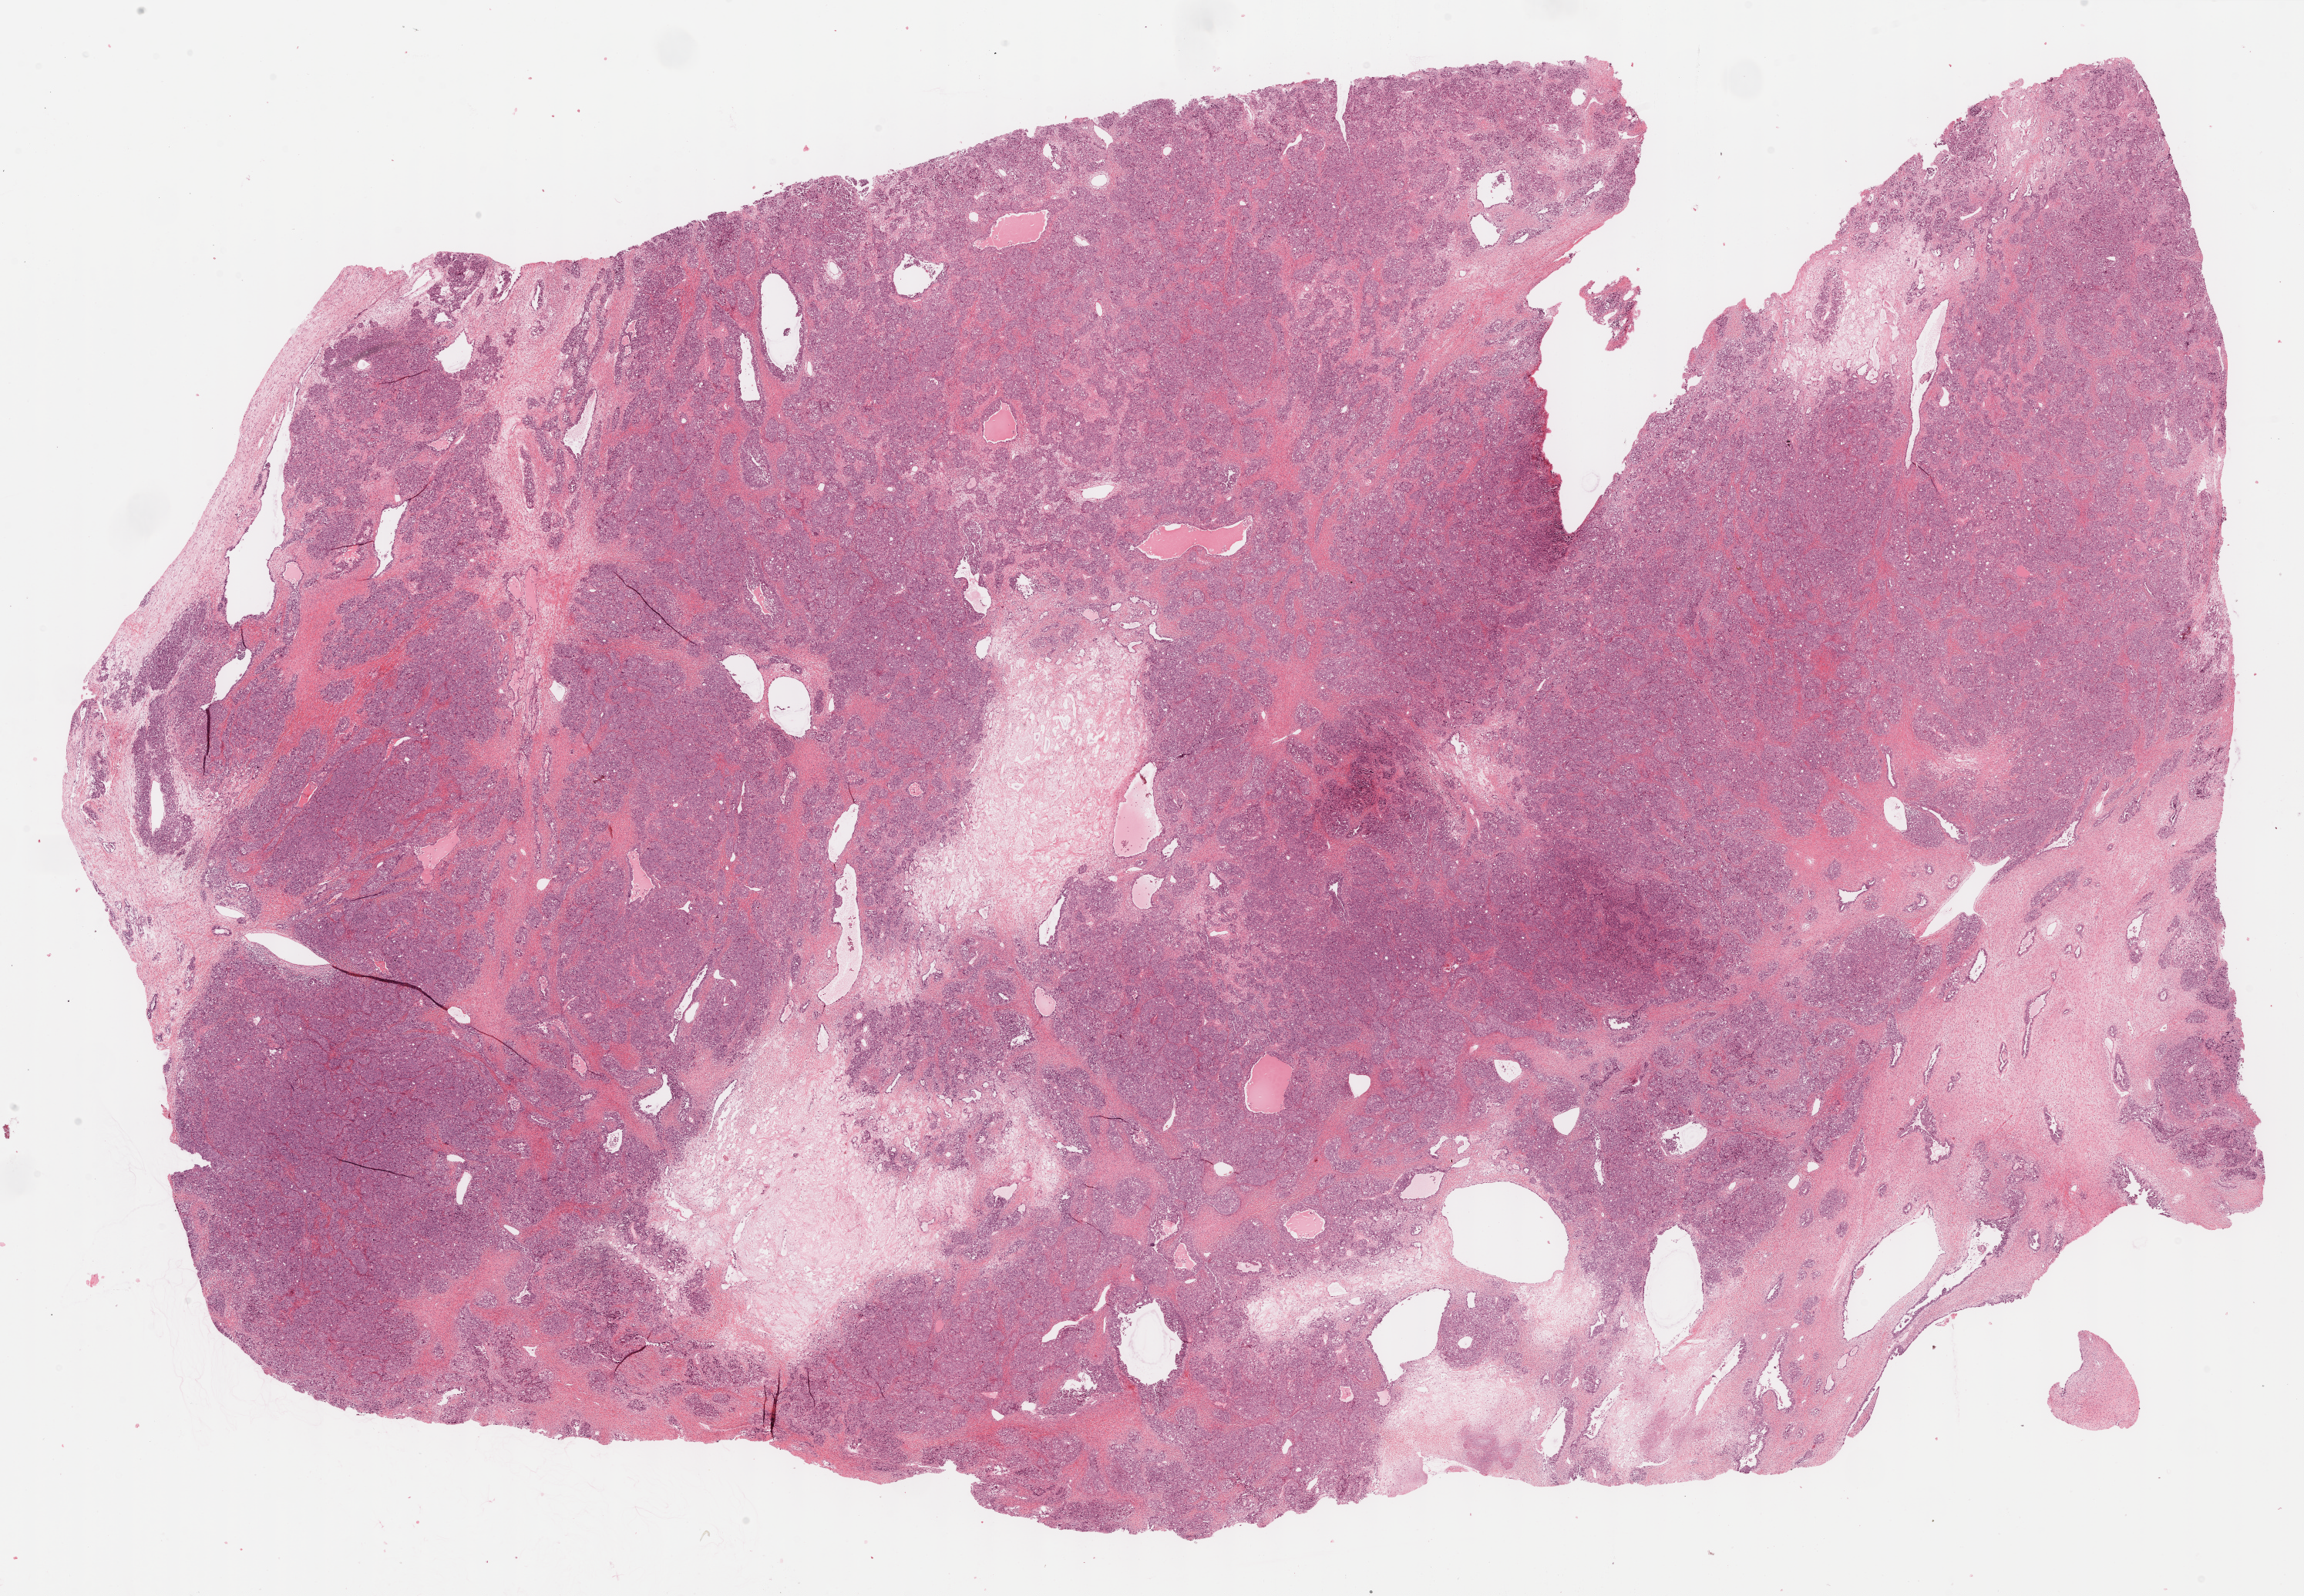
H&E-stained whole-slide image, whole scanned area (about 24.1 x 16.7 mm, slide scanned at 40x) shown as a low-resolution overview. FFPE section. Sample: primary tumour, ovary. Female patient; age at initial diagnosis 60 years.
Histologic diagnosis: Serous cystadenocarcinoma, NOS.